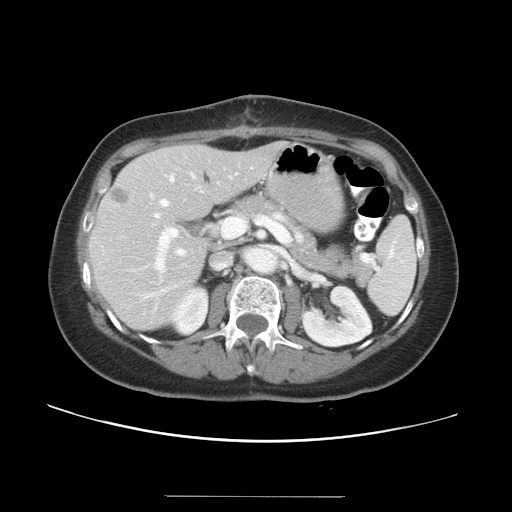
Contrast-enhanced abdominal CT, one axial slice; position 18 of 34 along the scan axis; reconstruction kernel STANDARD; 120 kVp; intravenous contrast given; soft-tissue window (W 400 / L 40 HU); 512 × 512 image matrix, field of view 382 × 382 mm. Female patient, age 69 years. From the clinical record (not read from this slice): diagnosis: colorectal cancer liver metastases, imaged before liver resection.
Outlined on this slice (manually delineated by an expert):
- hepatic veins: bounding box <144,175,185,298> (left, top, right, bottom; pixels)
- liver: <90,143,285,330>
- planned liver remnant (the part of the liver to remain after resection): <90,143,285,330>
- portal vein (with intrahepatic branches): <154,213,373,272>
- liver metastasis: <109,185,131,206>